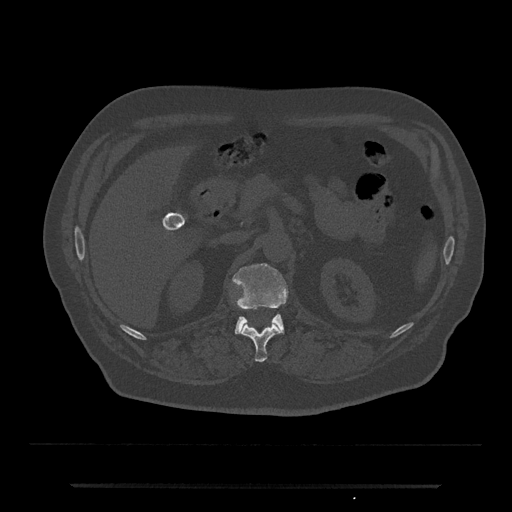
CT including the spine, one axial slice. Position 565 of 797 along the scan axis. Reconstruction kernel Br40s/3. 120 kVp. Bone window (W 1800 / L 400 HU). 0.5 mm slice thickness. 512 × 512 image matrix, field of view 434 × 434 mm. Patient: male, 80 years. From the clinical record (not read from this slice): primary cancer: prostate; vertebrae with lytic lesions (as recorded): L1, T11.
Structures marked on this image (semi-automatically segmented with operator editing):
- L1 vertebra: bounding box <232,263,288,334> (left, top, right, bottom; pixels)
- T12 vertebra: <242,324,281,362>